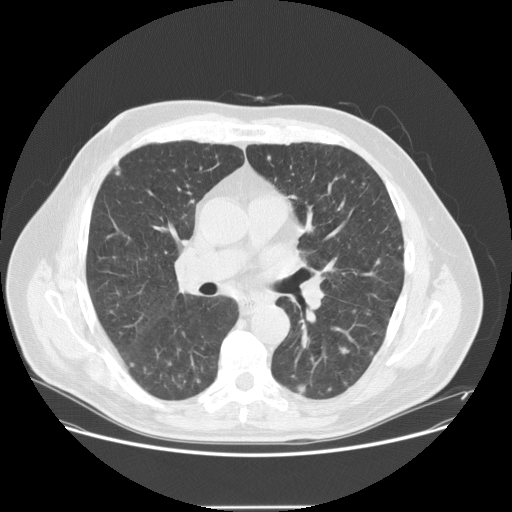
Low-dose screening chest CT, one axial slice. Position 82 of 143 along the scan axis. 120 kVp. Lung window (W 1500 / L -600 HU). 2.5 mm slice thickness. 512 × 512 image matrix.
Annotated regions visible in this slice (outlined manually by an expert reader):
- lesion 5 (tumor): bounding box <297,385,306,394> (left, top, right, bottom; pixels)